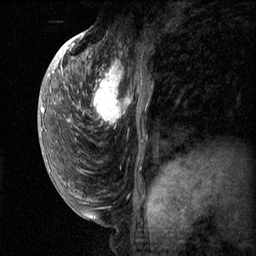
Breast MRI (dynamic contrast-enhanced), one sagittal slice. Dynamic contrast-enhanced series, image 2 of 3 at this slice position (ordered by acquisition). 1.5 T. TE 4.2 ms, TR 11.1 ms. 2 mm slice thickness. 256 × 256 image matrix, field of view 180 × 180 mm. Patient: female, 50 years.
Outlined on this slice (semi-automatic segmentation, software-assisted and operator-edited):
- analysis volume of interest (the breast-tissue region the enhancement analysis was run in; not a lesion): bounding box [x1, y1, x2, y2] px = [82, 56, 151, 143]
- tumour enhancement mask (voxels above the 70 % enhancement threshold inside the analysis volume of interest): [83, 56, 146, 127]